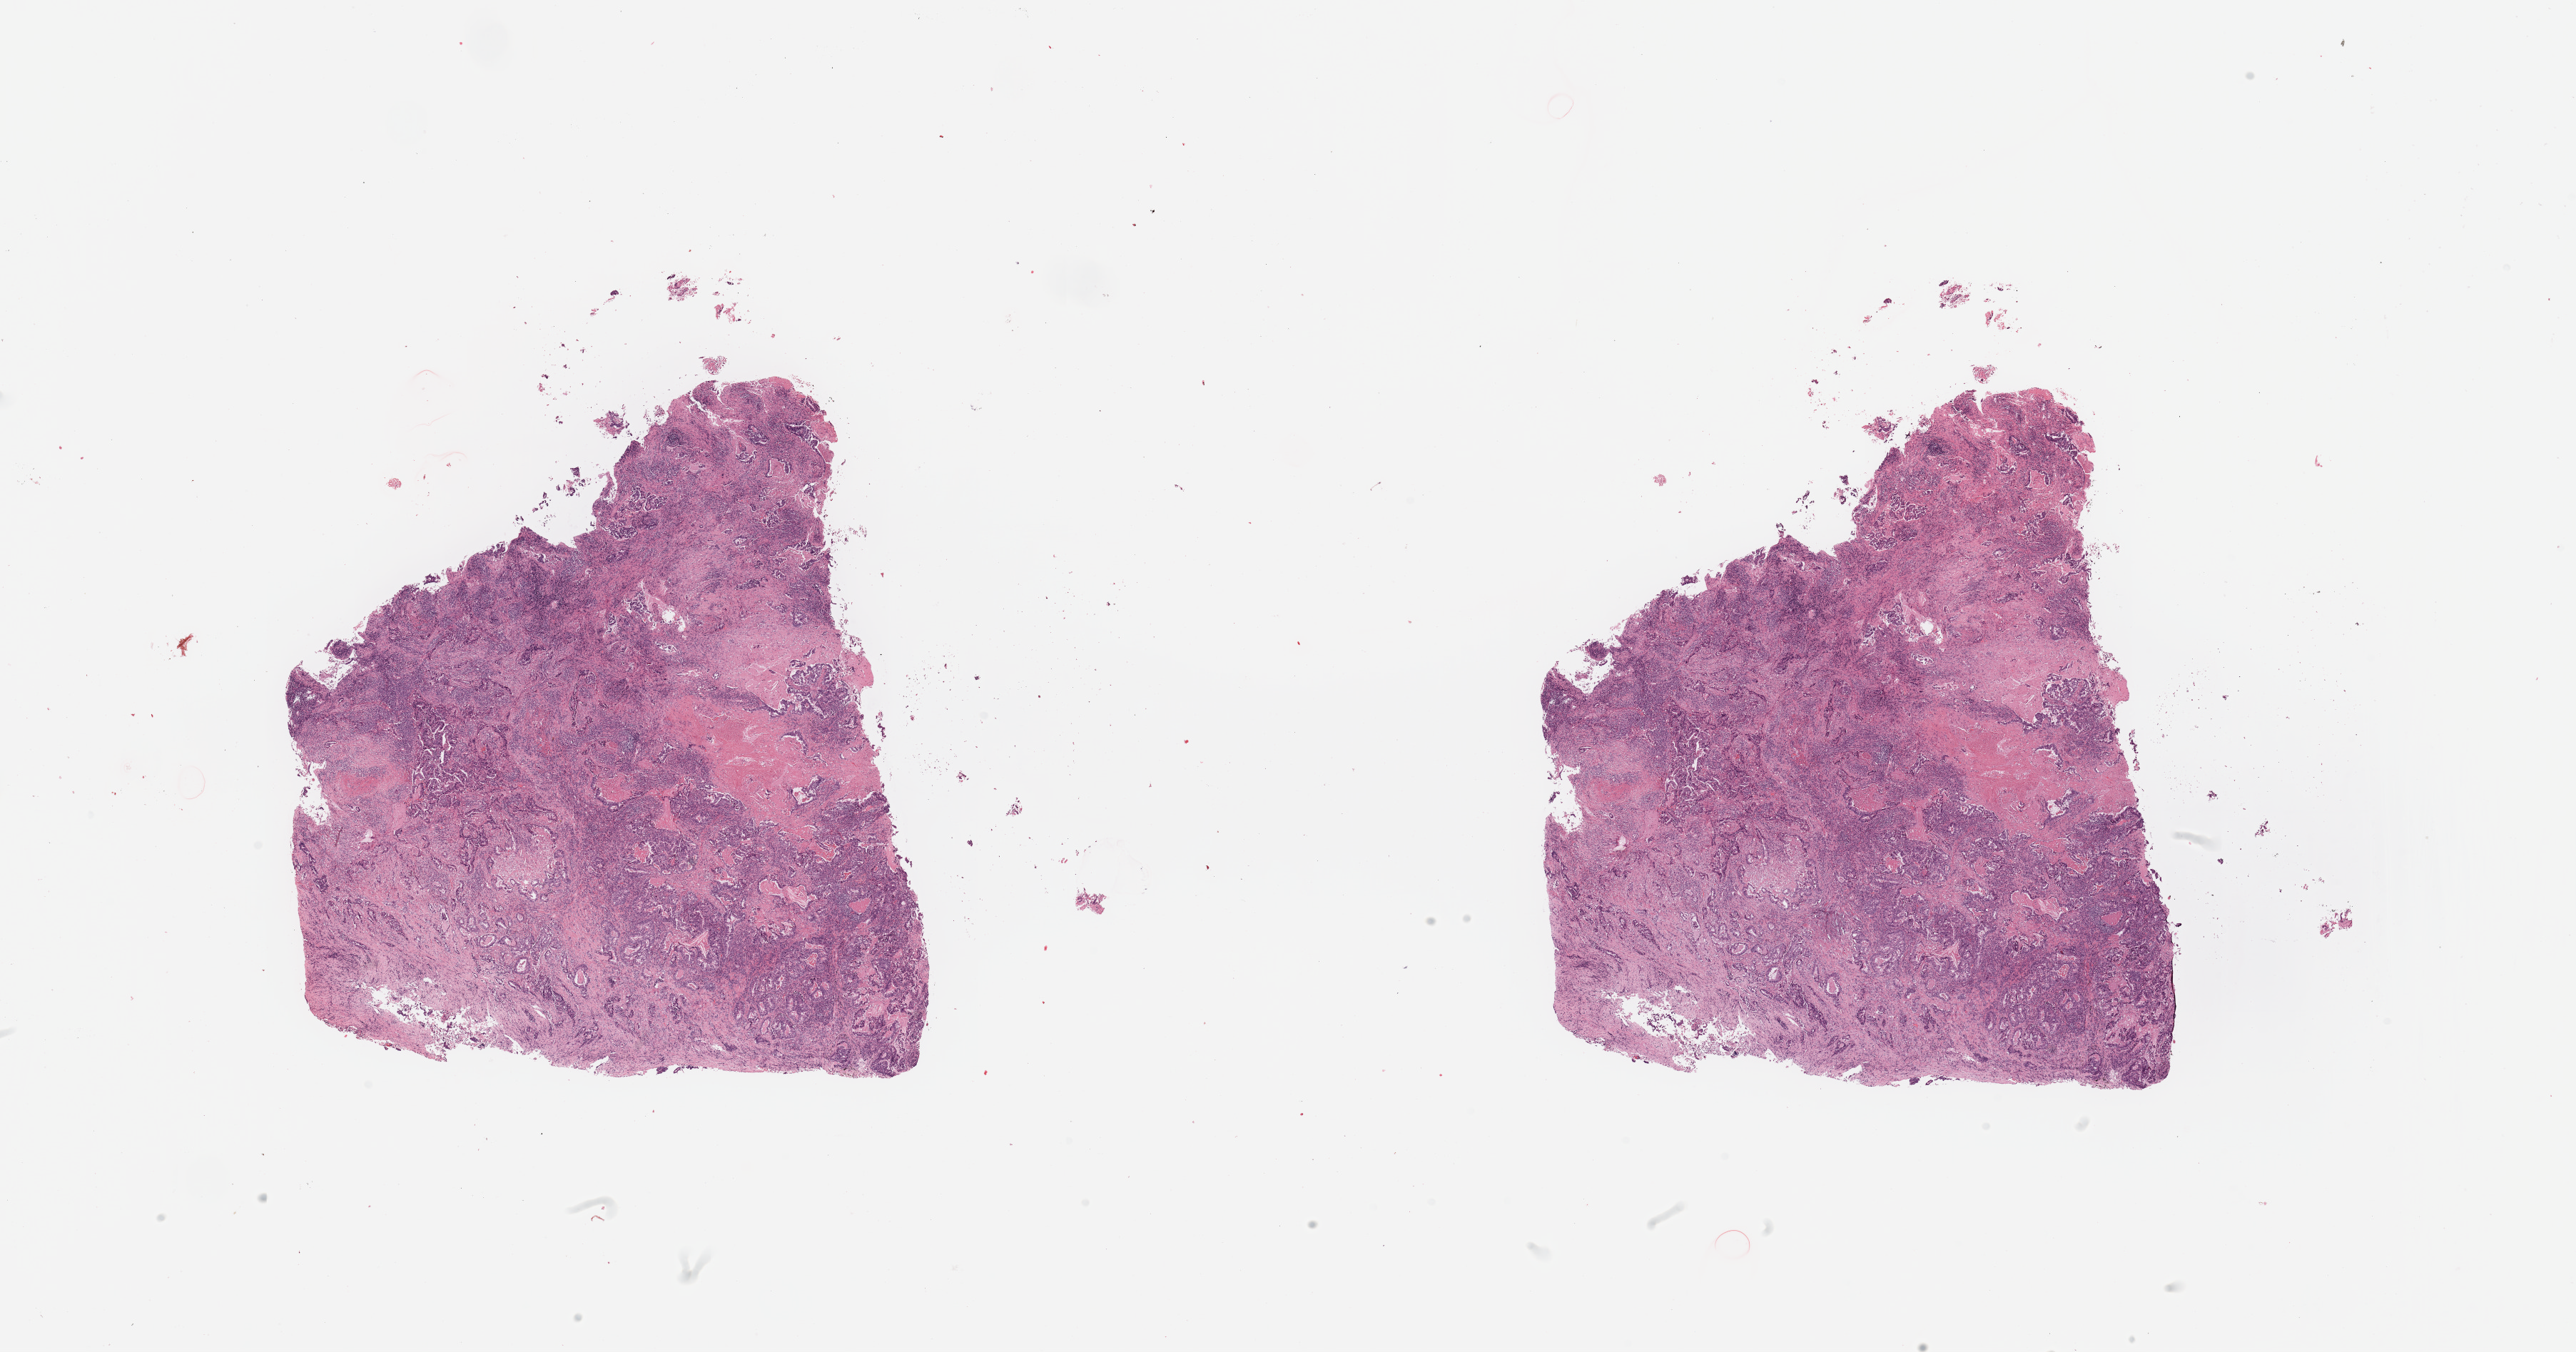
Hematoxylin and eosin (H&E) stained whole-slide image, a low-resolution overview of the entire scanned area, about 28.5 x 15.0 mm (acquisition: 20x scan); tumour tissue sample, lung. Male, 63 y/o. Histologic grade: G2 (moderately differentiated).
Primary tumour site (as recorded): right middle lobe. AJCC pathologic stage: IIA. Histologic diagnosis: Adenocarcinoma, NOS.